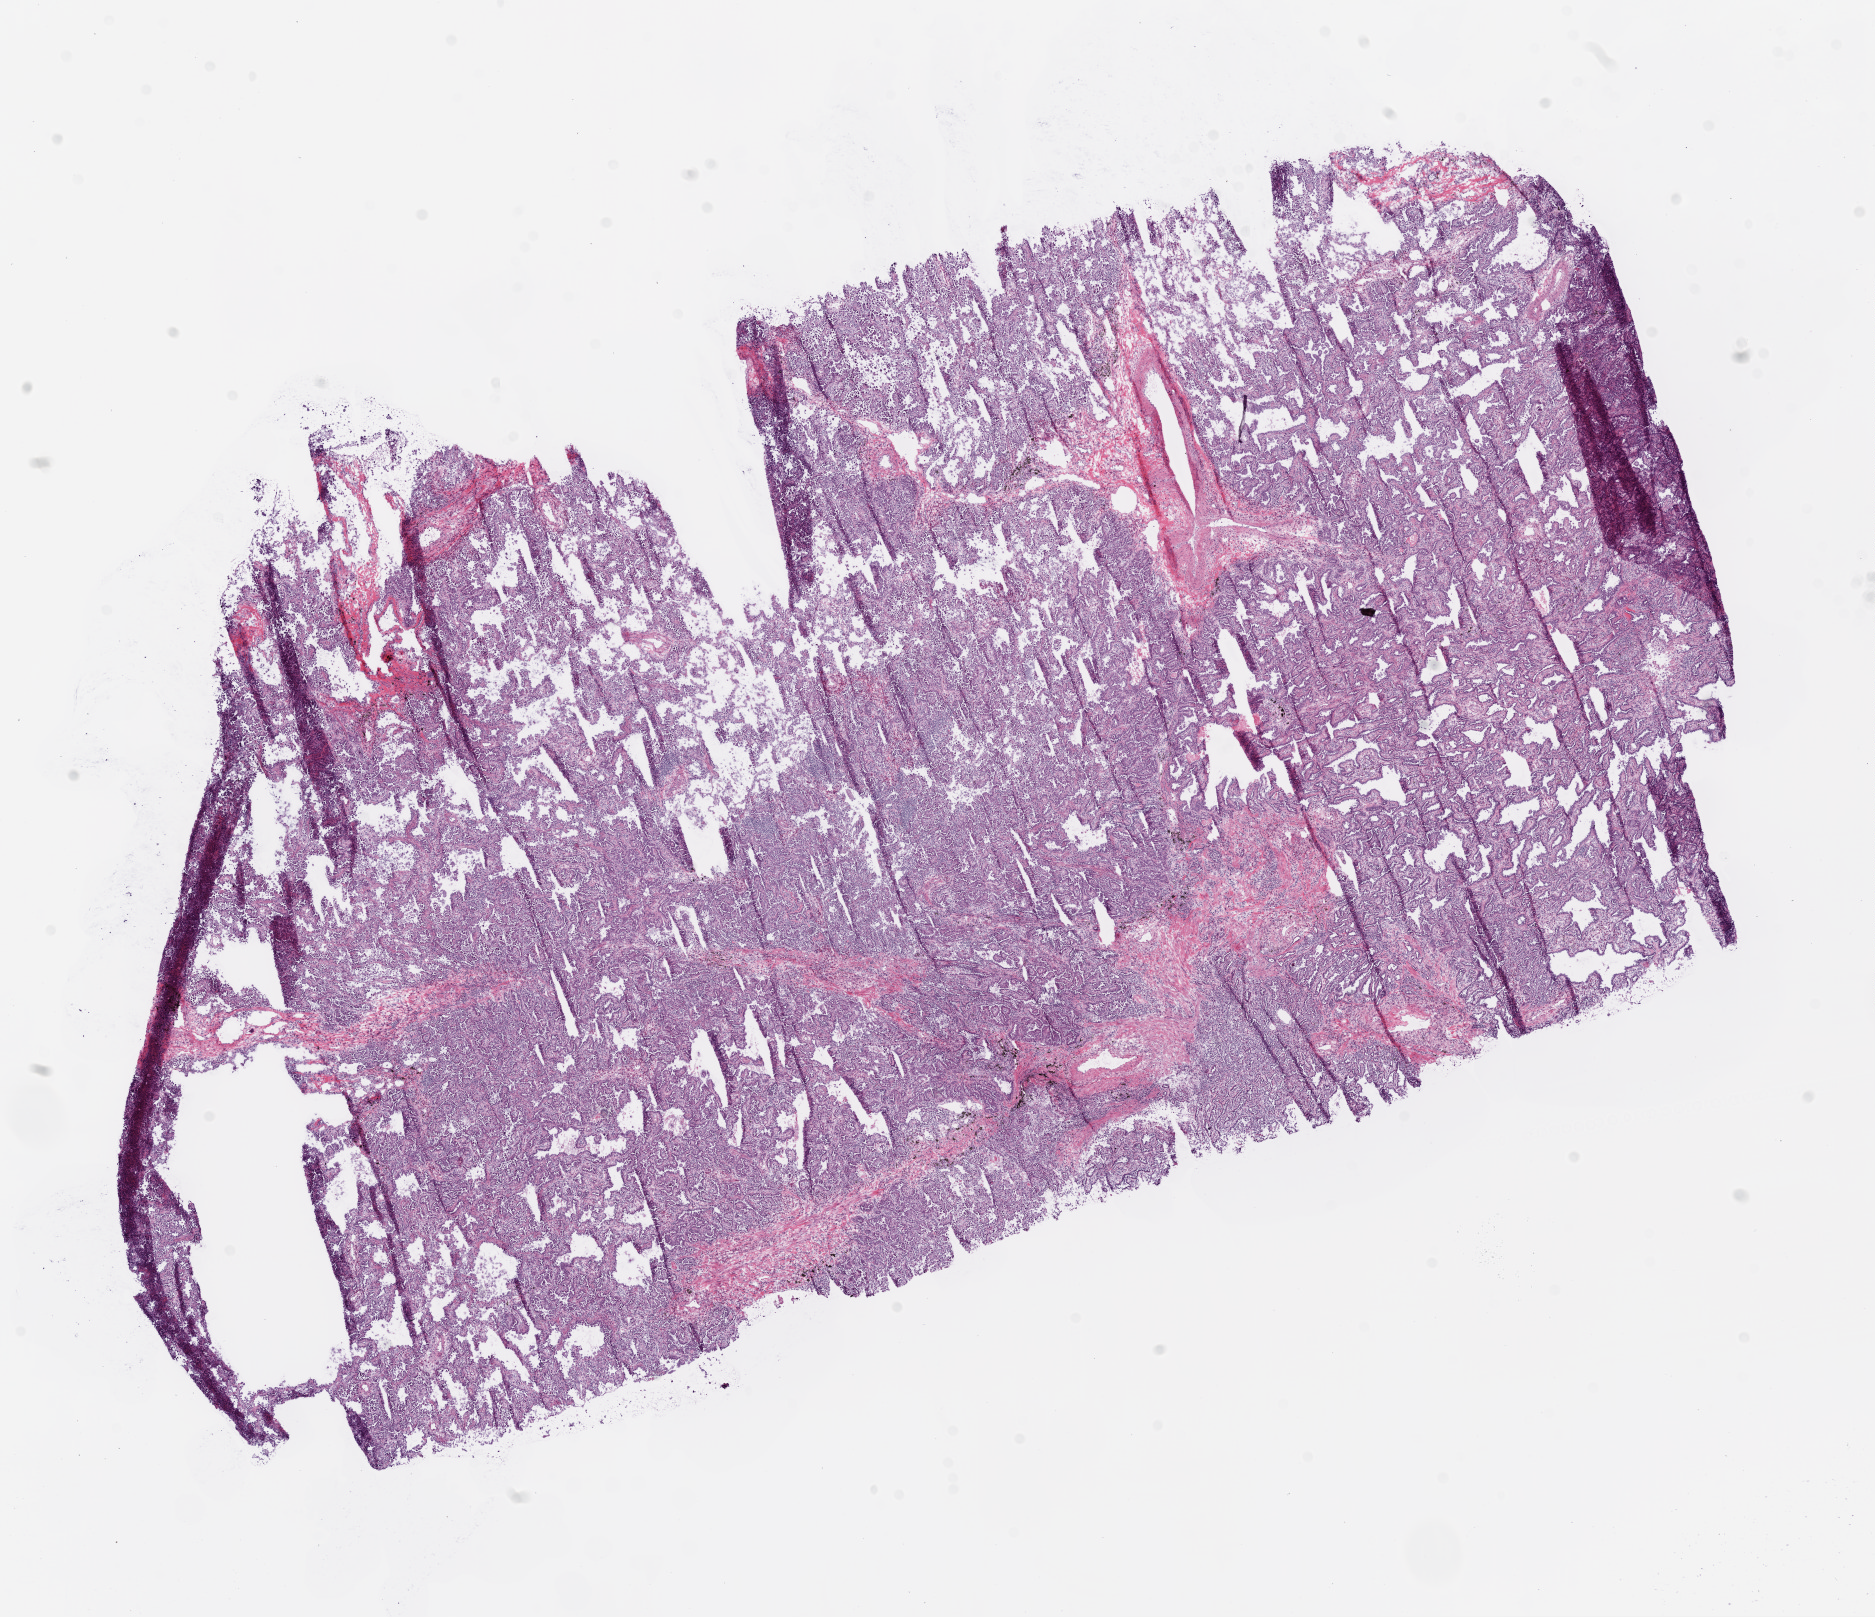
H&E-stained whole-slide image, shown as a low-resolution overview of the whole scanned area (about 15.0 x 13.0 mm), frozen section, lung, primary tumour sample. Male patient; age at initial diagnosis 43 years. Composition of this section per pathologist review: tumour cells 90%, tumour nuclei 90%, normal cells 0%, stromal cells 9%, necrosis 1%. Infiltration values recorded for this section: lymphocyte infiltration 2%.
- AJCC pathologic stage: IB
- histologic diagnosis: Adenocarcinoma, NOS (upper lobe, lung)
- laterality: right